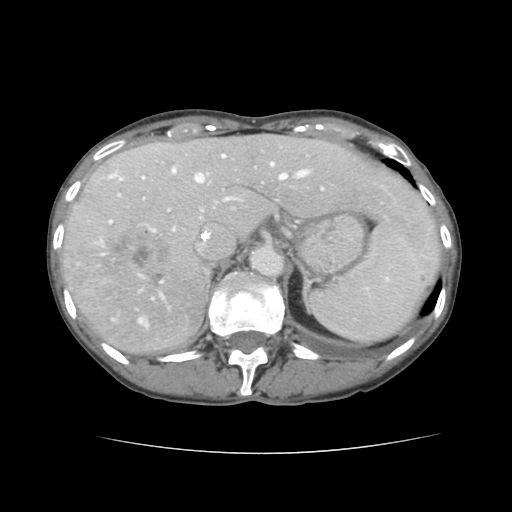
Contrast-enhanced abdominal CT, one axial slice; slice 103 of 136 in the series (ordered by position); 120 kVp; intravenous contrast given; soft-tissue window (W 400 / L 40 HU); 2.5 mm slice thickness; 512 × 512 image matrix. Female patient, age 77 years. Case-level facts recorded for this patient, not image findings: diagnosis: colorectal cancer liver metastases, imaged before liver resection; multiple liver metastases: yes.
Outlined on this slice (outlined manually by an expert reader):
- hepatic veins: bounding box [x1, y1, x2, y2] px = [98, 154, 307, 327]
- liver: [64, 136, 439, 356]
- planned liver remnant (the part of the liver to remain after resection): [159, 136, 439, 265]
- portal vein (with intrahepatic branches): [109, 172, 383, 223]
- liver metastasis: [100, 226, 176, 296]